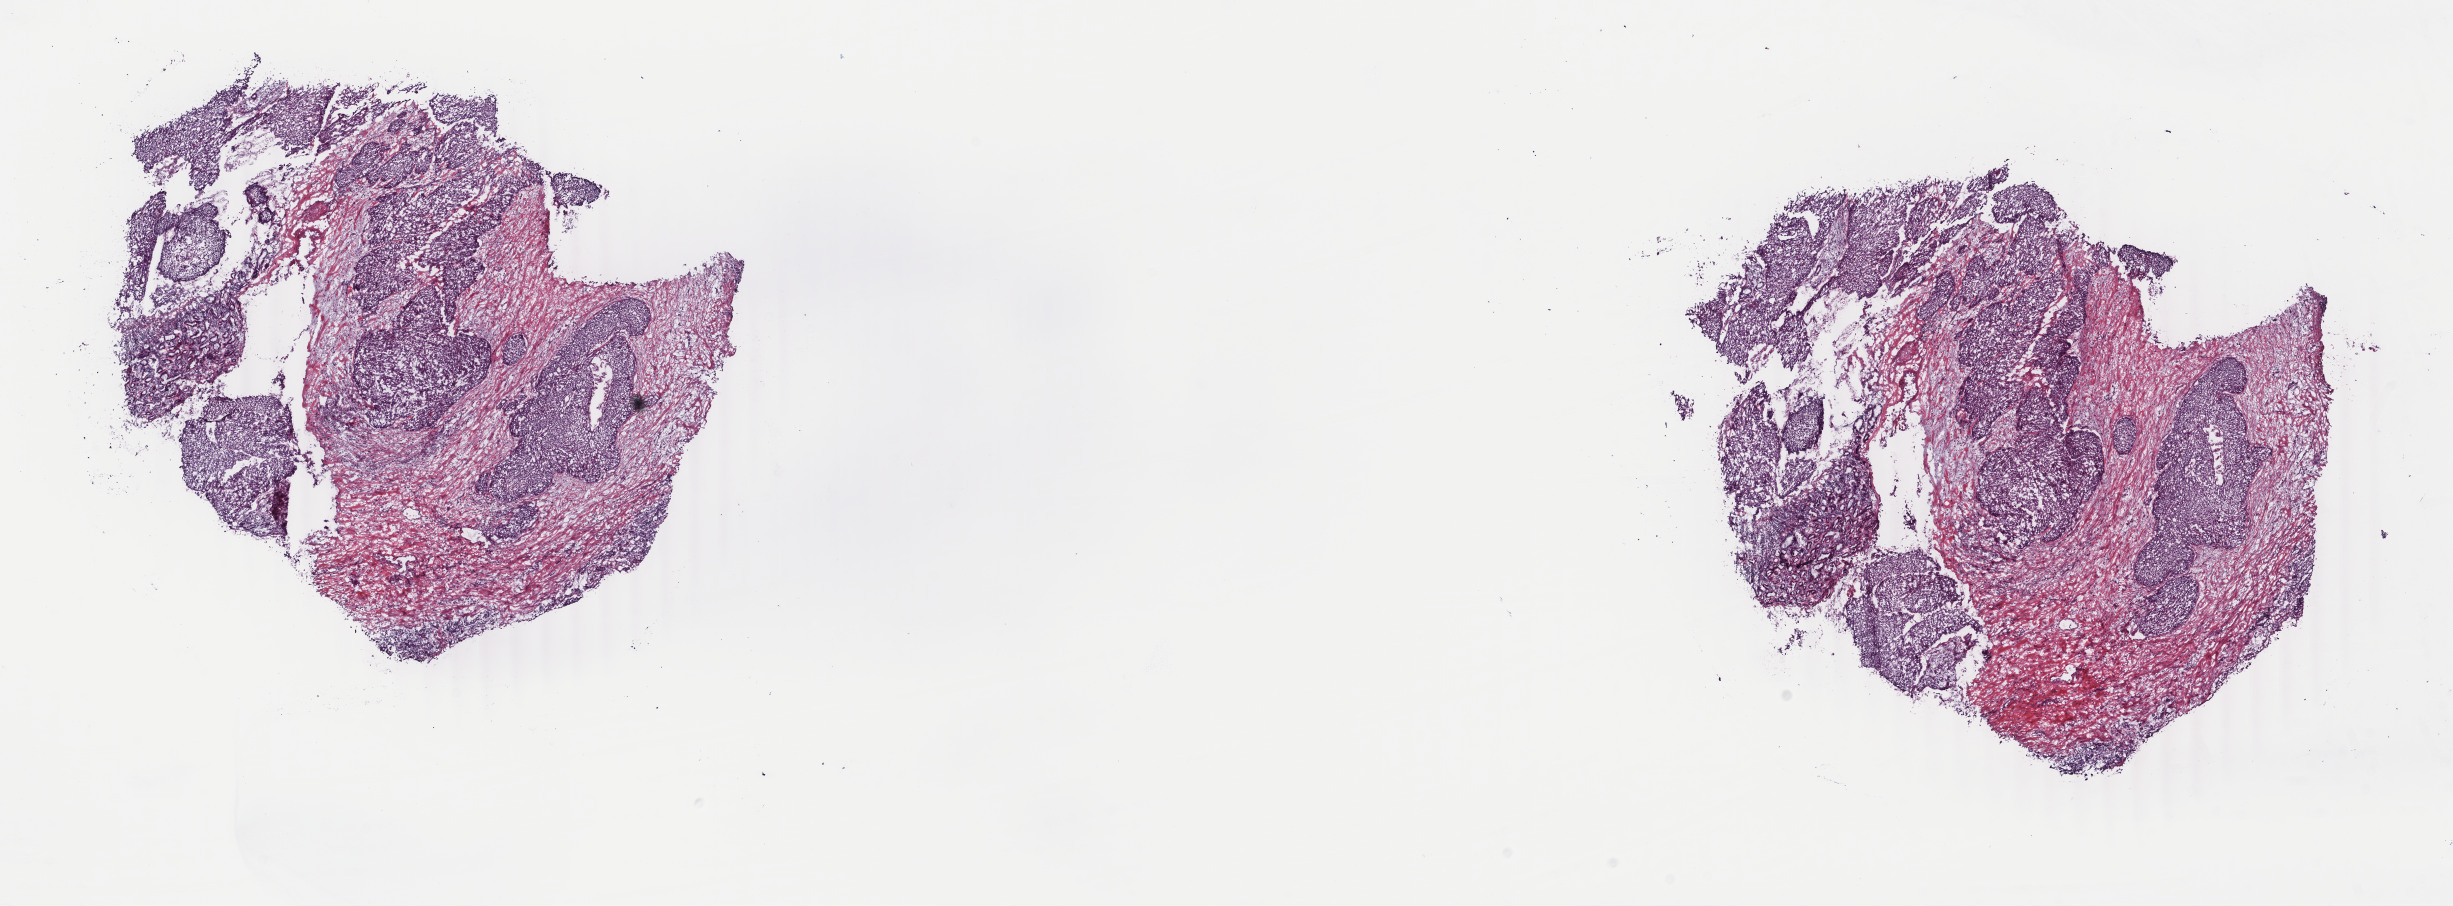
H&E-stained whole-slide image — low-resolution overview of the scanned area, about 19.5 x 7.2 mm (slide scanned at 40x), frozen section from the top of the tissue portion, primary tumour sample from the lung. Male, age 69 years at initial diagnosis. Composition of this section per pathologist review: tumour cells 95%, tumour nuclei 70%, normal cells 0%, stromal cells 5%, necrosis 0%. Inflammatory infiltration, as recorded: lymphocyte infiltration 0%, monocyte infiltration 0%, neutrophil infiltration 0%.
Histologic diagnosis: Squamous cell carcinoma, NOS (overlapping lesion of lung). AJCC pathologic stage: IIIA (7th edition).